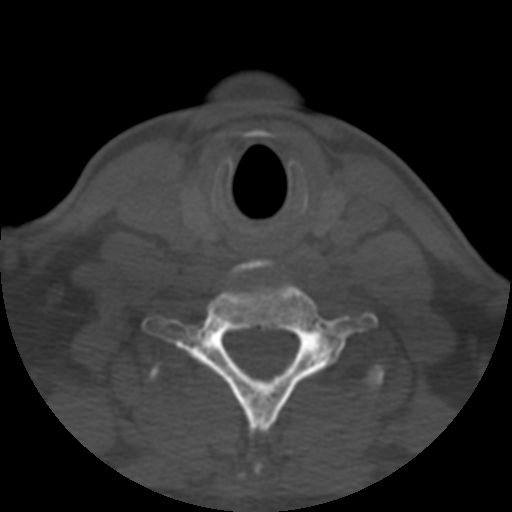
CT including the spine, one axial slice; slice 463 of 508 in the series (ordered by position); reconstruction kernel STANDARD; bone window (W 1800 / L 400 HU); 512 × 512 image matrix, field of view 160 × 160 mm. Patient age 57 years. From the clinical record (not read from this slice): primary cancer: prostate.
Structures marked on this image (semi-automatically segmented with operator editing):
- T1 vertebra: box from (x=150, y=365) to (x=384, y=385) px